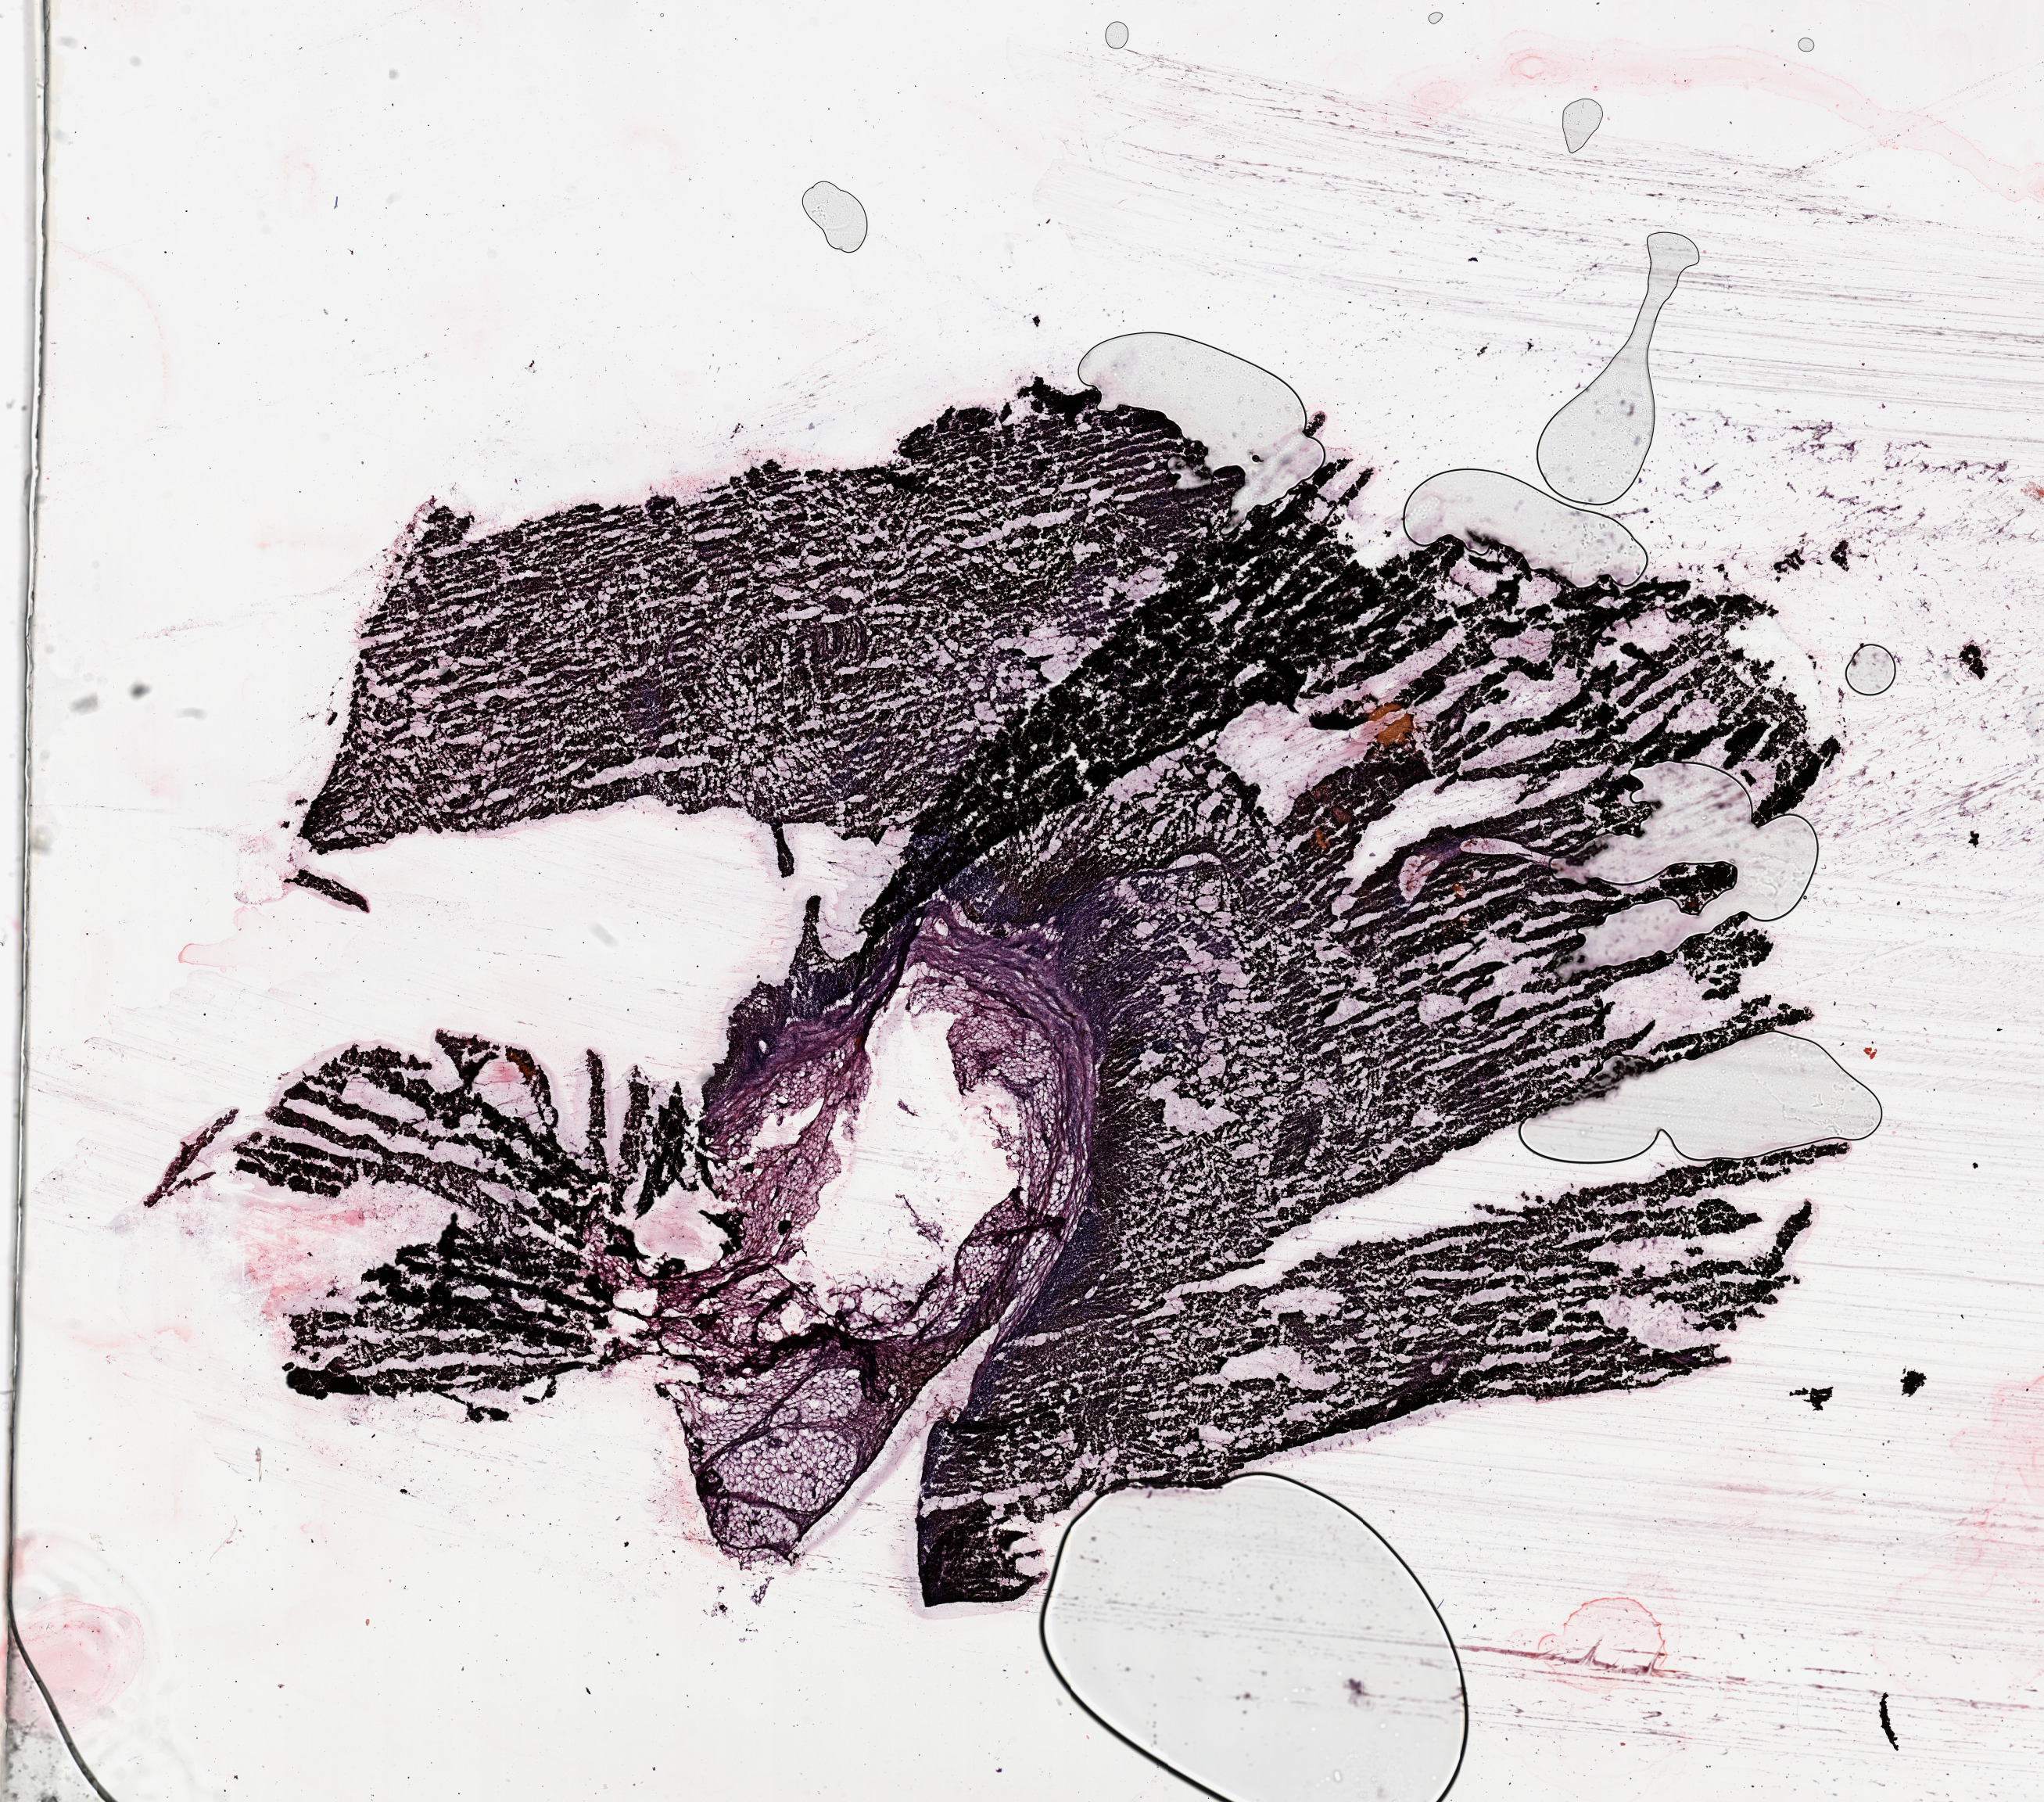
H&E-stained whole-slide image — shown as a low-resolution overview of the whole scanned area (about 20.7 x 18.2 mm, from a 20x scan). Melanoma tumour tissue; sampled site not recorded. 74-year-old female patient.
Primary tumour site (as recorded): trunk. Patient diagnosis (cohort enrolment): cutaneous melanoma (skin).